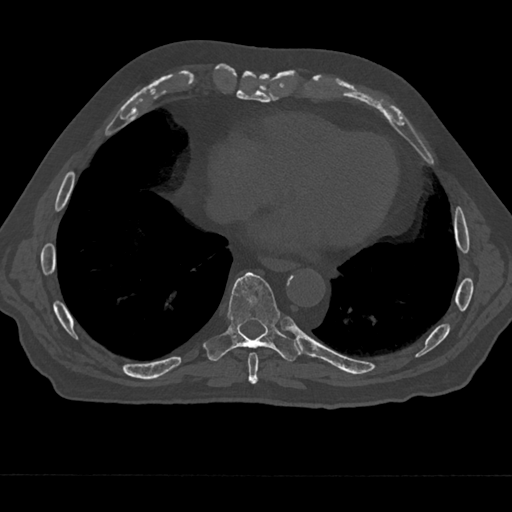
CT including the spine, one axial slice. 120 kVp. Bone window (W 1800 / L 400 HU). 0.5 mm slice thickness. 512 × 512 image matrix, field of view 377 × 377 mm. Male patient, age 75 years. From the clinical record (not read from this slice): primary cancer: renal; vertebrae with lytic lesions (as recorded): T4.
Structures marked on this image (semi-automatically segmented with operator editing):
- T8 vertebra: bounding box (x1, y1, x2, y2) in pixels: (248, 352, 259, 384)
- T9 vertebra: (204, 272, 301, 362)